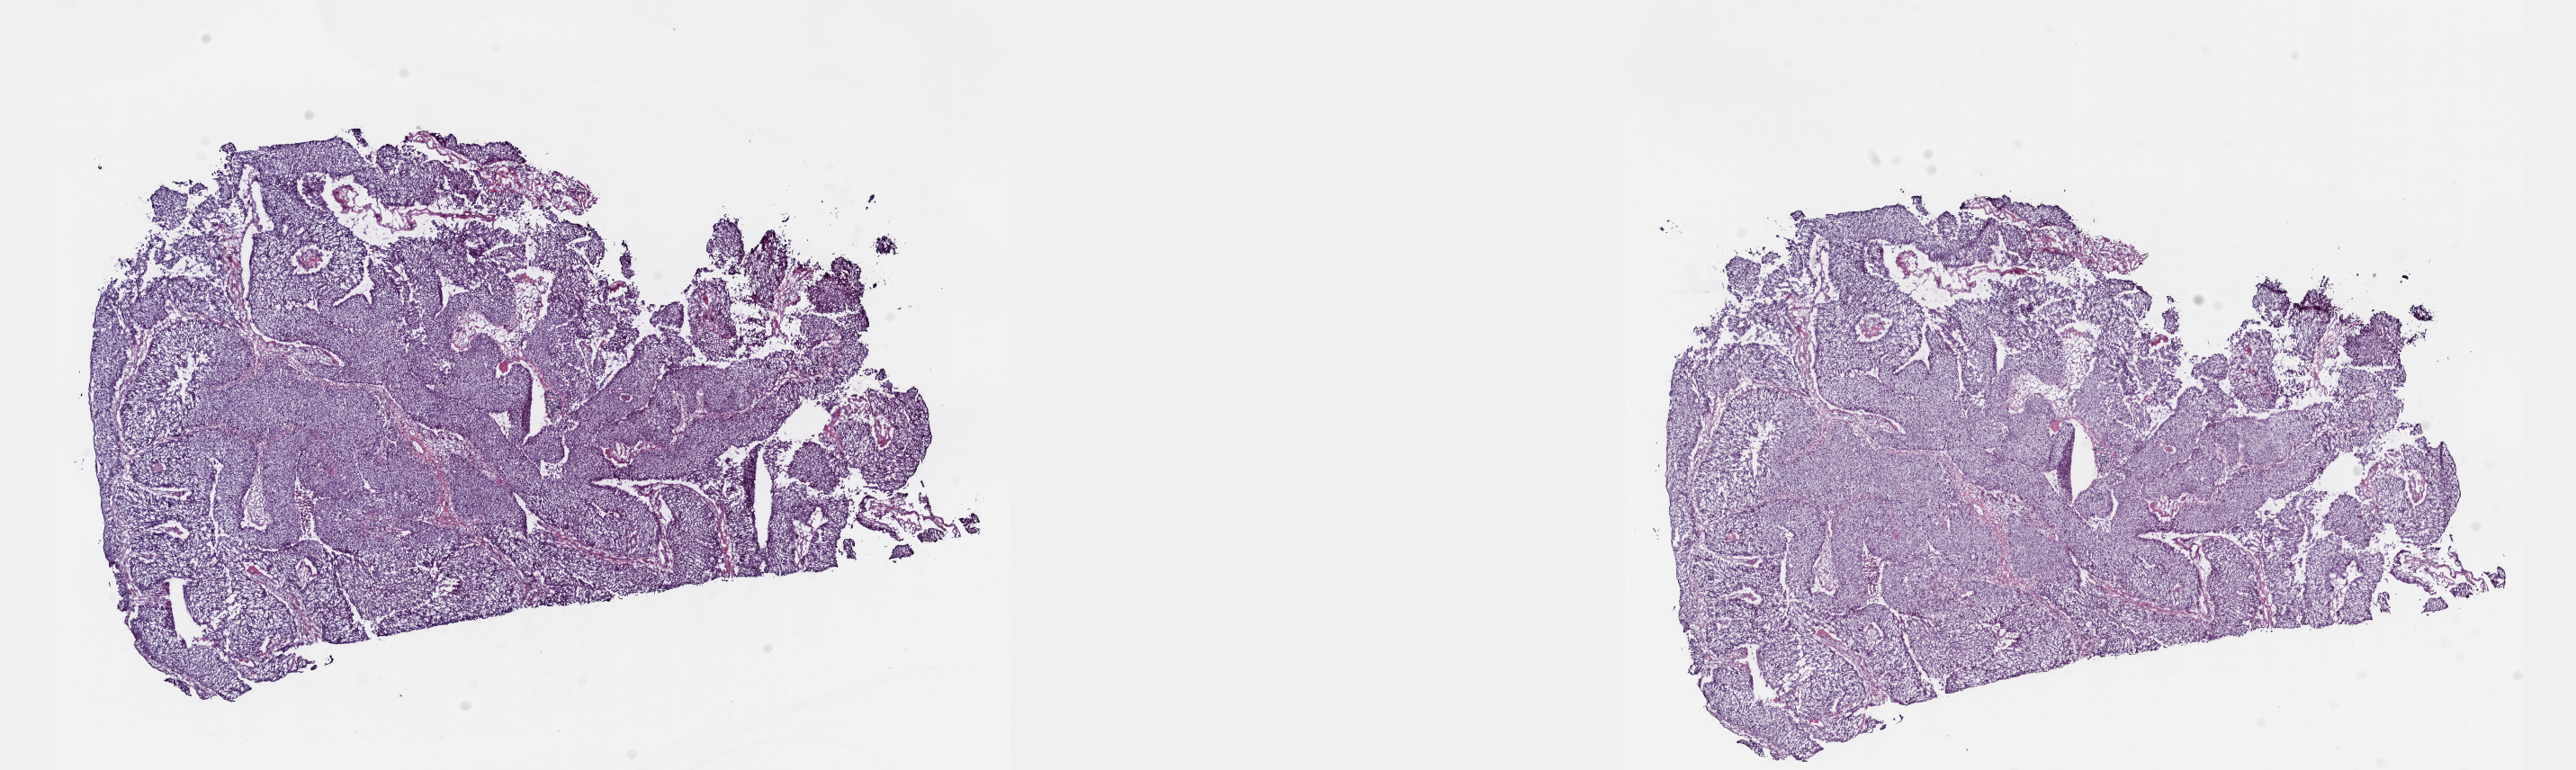
Whole-slide histology image, H&E-stained — whole scanned area (about 23.1 x 6.9 mm, slide scanned at 40x) shown as a low-resolution overview, frozen section from the top of the tissue portion, bladder, primary tumour sample. Male patient; age at initial diagnosis 61 years. Histologic grade: high grade. Pathologist review of this section (percent, as recorded): tumour cells 100%, tumour nuclei 75%, normal cells 0%, stromal cells 0%, necrosis 0%. Infiltration values recorded for this section: lymphocyte infiltration 3%, monocyte infiltration 0%, neutrophil infiltration 0%.
TNM: T2a N0 M0. AJCC pathologic stage: II. Histologic diagnosis: Transitional cell carcinoma (posterior wall of bladder).